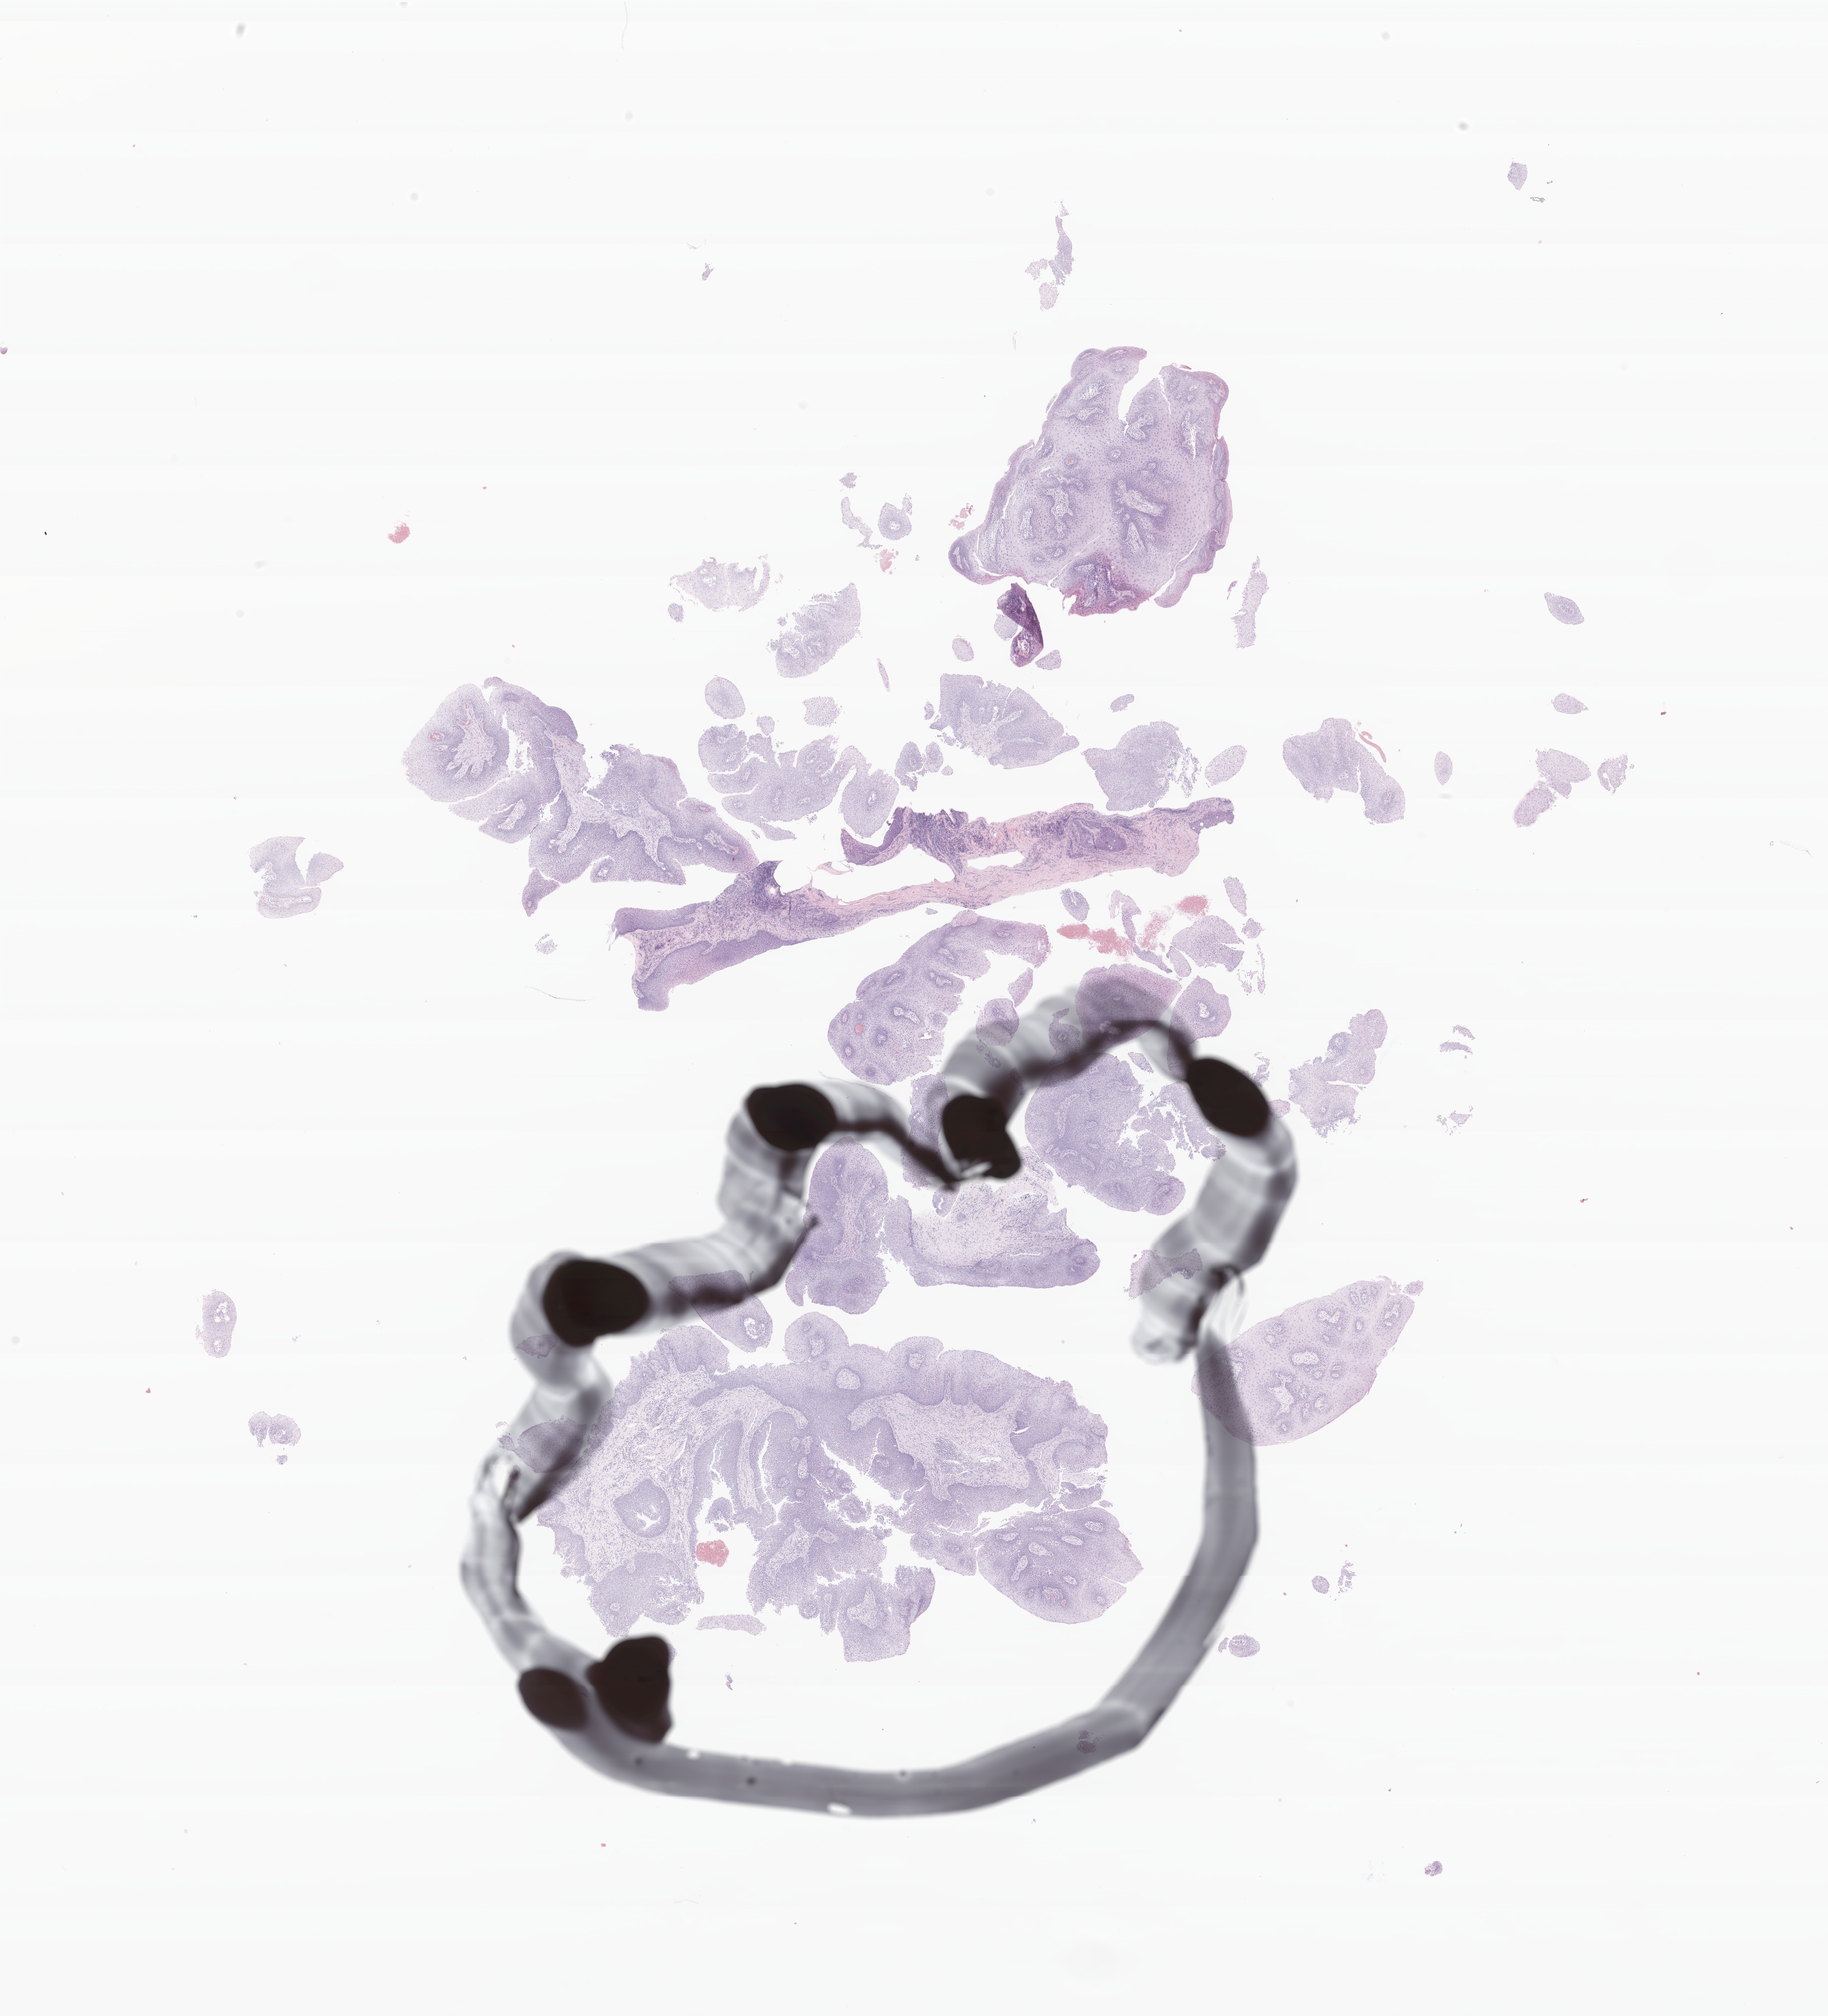
Digitized haematoxylin and eosin-stained section of tumor tissue from the larynx — whole scanned area (about 17.5 x 19.4 mm) shown as a low-resolution overview, FFPE section. Female patient, age 297 months (24 years 9 months).
Diagnosis (ICD-O-3 morphology term): Carcinoma in situ, NOS.